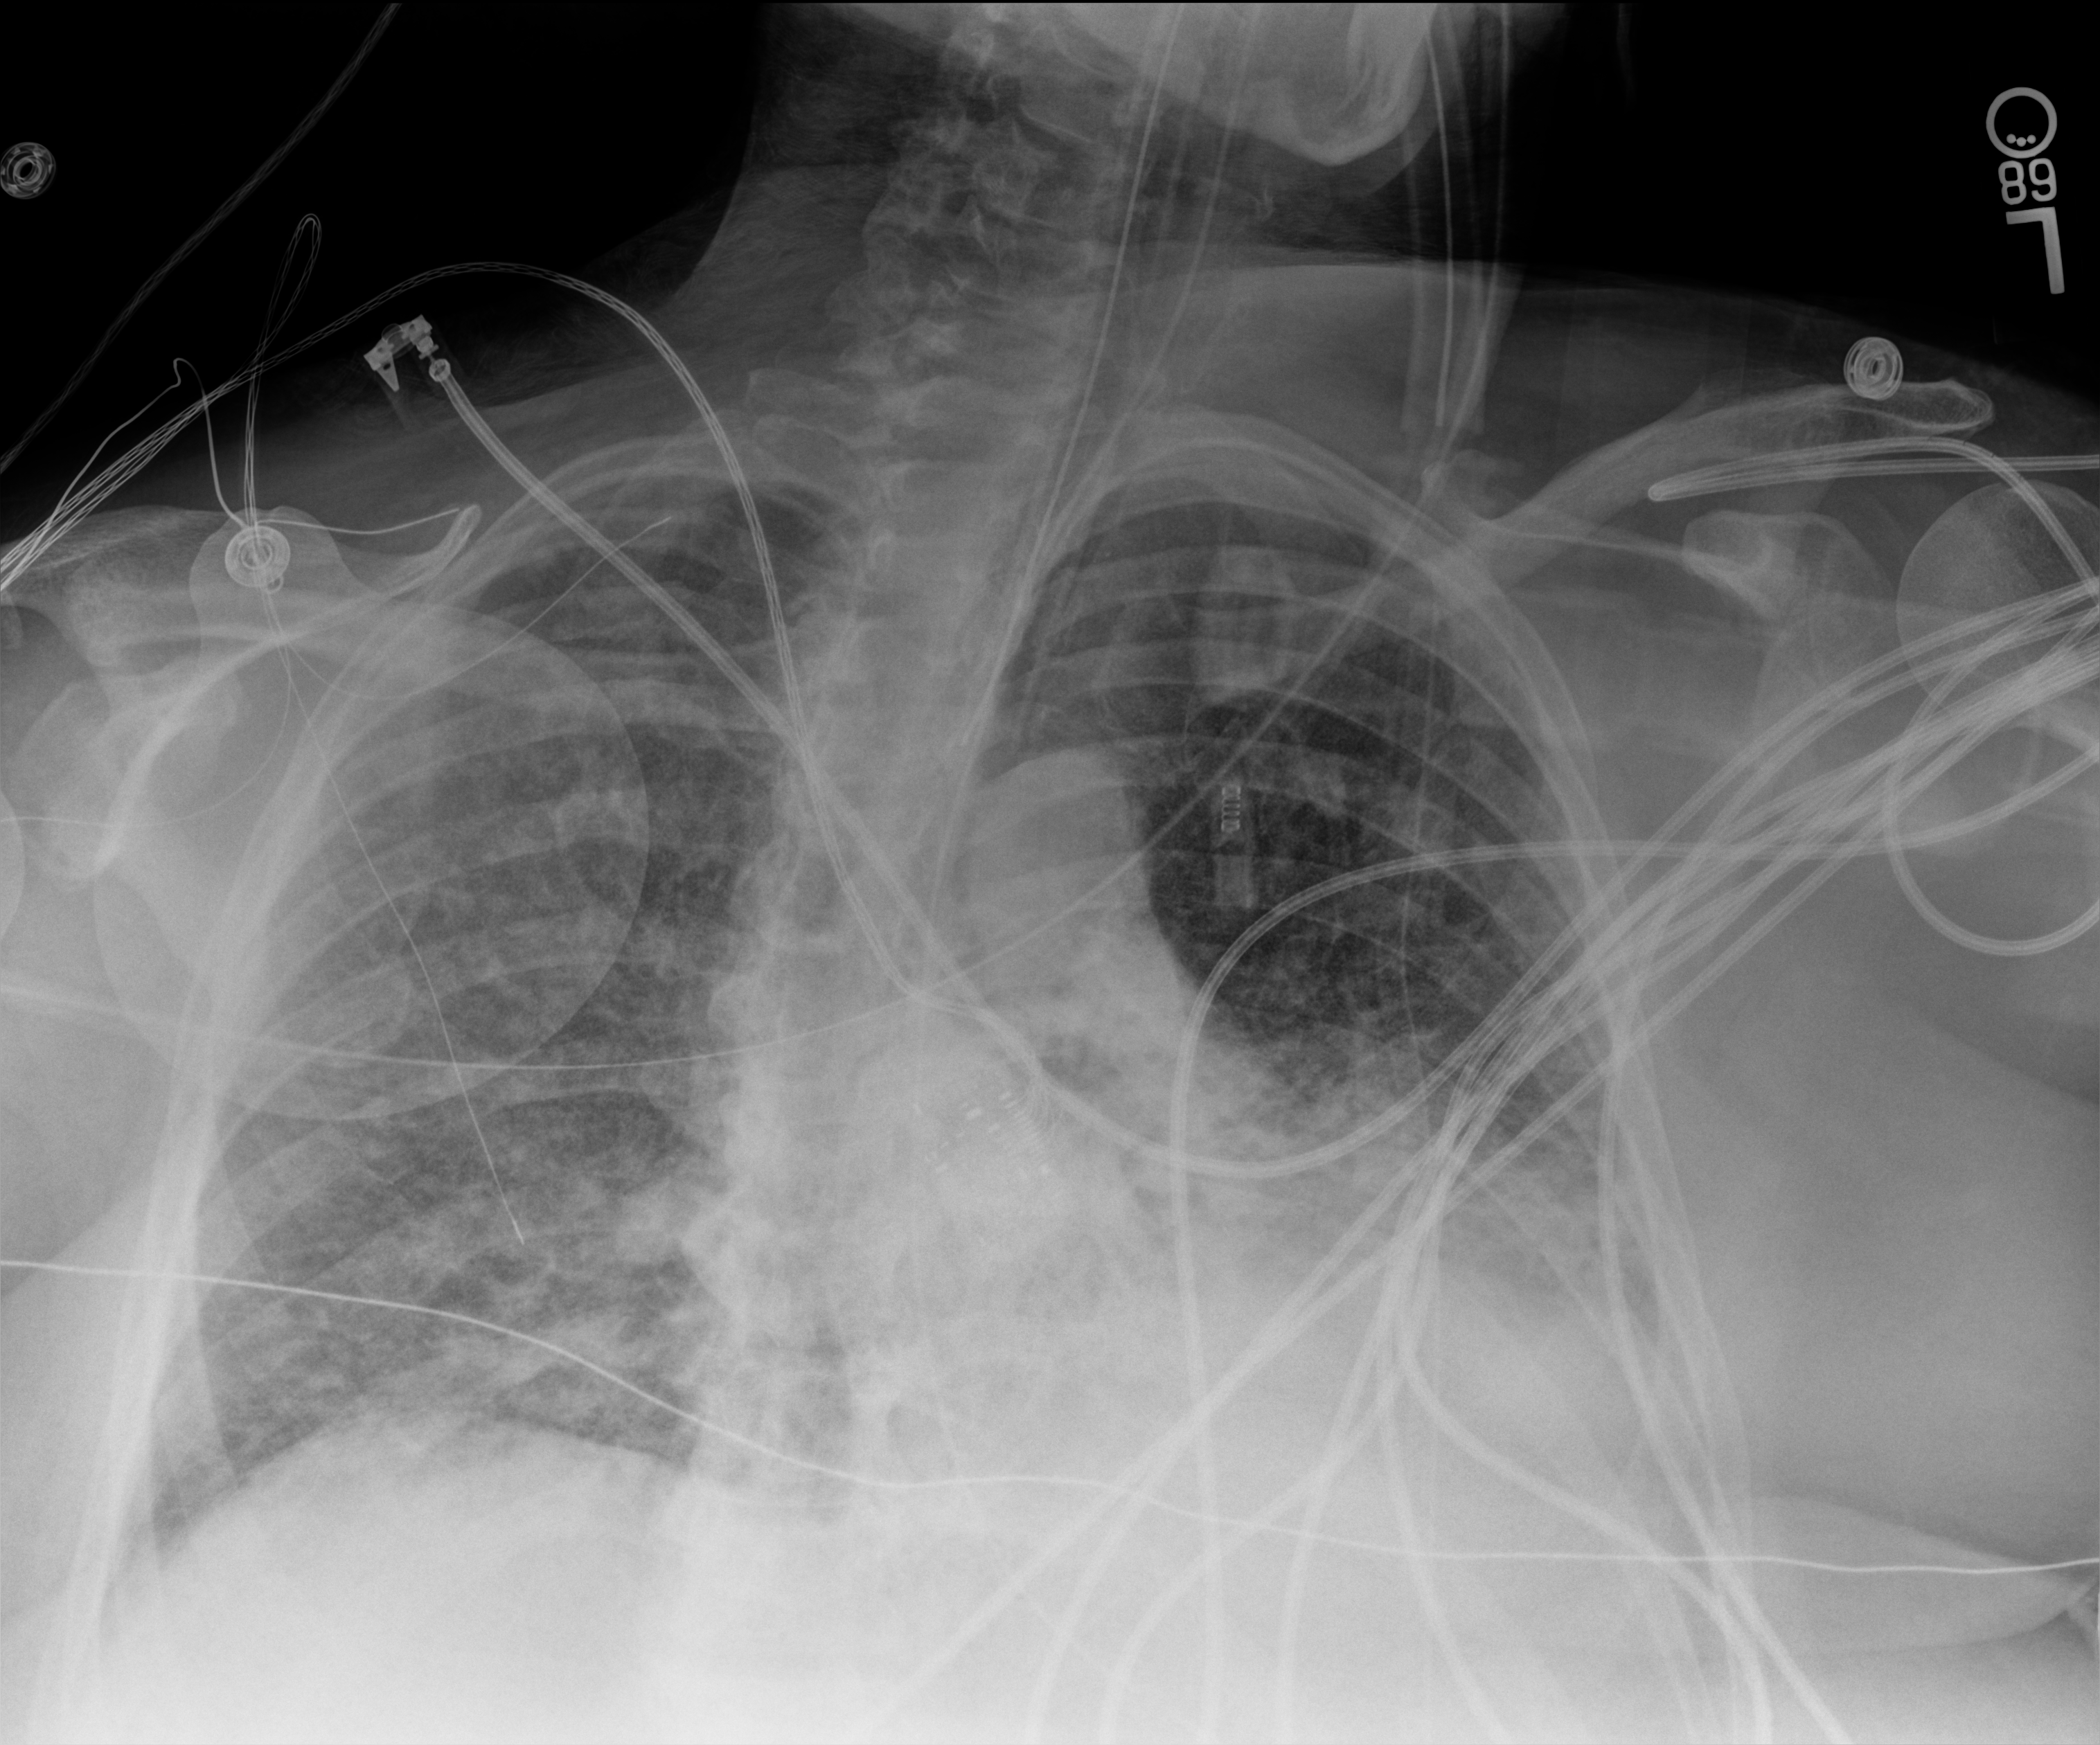
Chest X-ray (portable). Patient hospitalised with COVID-19, aged 18–59 years.
Hospital-stay facts (about this admission, not read from this image; timing relative to this image not recorded): length of hospital stay: 28 days; mechanically ventilated during this hospital stay: yes; admitted to intensive care during this hospital stay: yes.